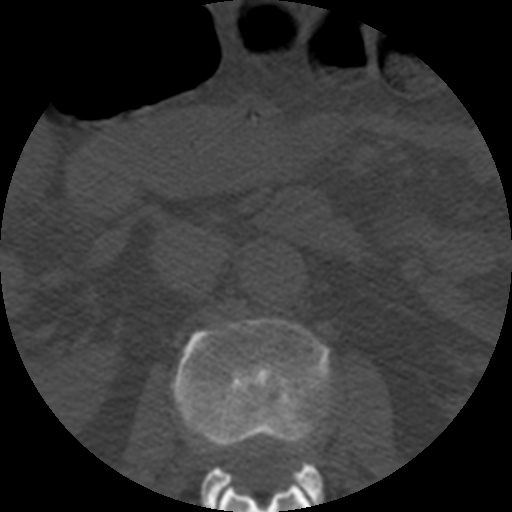
CT including the spine, one axial slice. Position 167 of 508 along the scan axis. Reconstruction kernel STANDARD. 120 kVp. Bone window (W 1800 / L 400 HU). 512 × 512 image matrix, field of view 160 × 160 mm. Patient age 57 years. Case-level facts recorded for this patient, not image findings: primary cancer: prostate.
Structures marked on this image (semi-automatic segmentation, software-assisted and operator-edited):
- L1 vertebra: bounding box (x1, y1, x2, y2) in pixels: (219, 481, 312, 512)
- L2 vertebra: (172, 318, 332, 512)